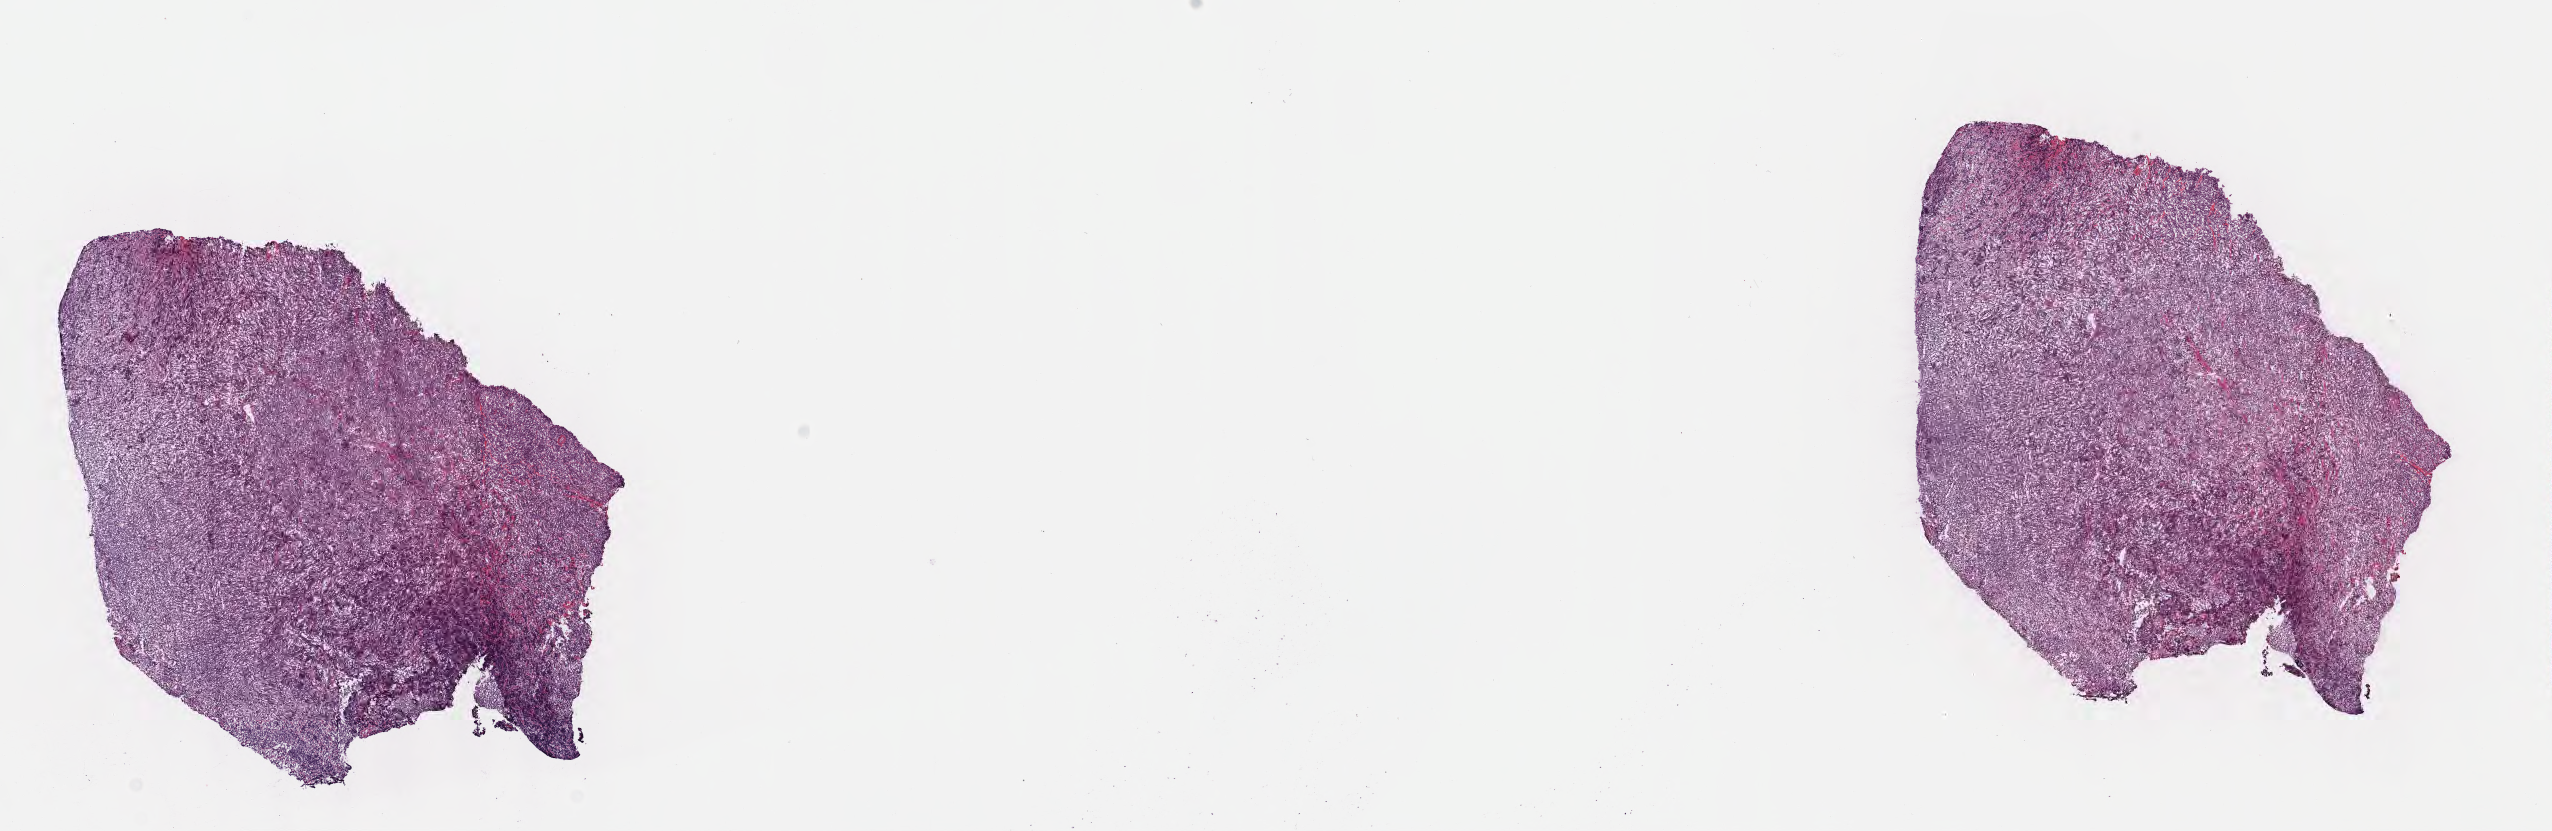
Digitized haematoxylin and eosin-stained section — shown as a low-resolution overview of the whole scanned area (about 20.6 x 6.7 mm). Frozen section. Specimen: primary tumor. Anatomic site: head and neck. Male patient; age at initial diagnosis 4 years. Pathologist review of this section (percent, as recorded): tumor cells 90%, tumor nuclei 95%, stromal cells 10%, necrosis 0%, normal cells 0%. Inflammatory infiltration, as recorded: lymphocyte infiltration 80%, monocyte infiltration 10%, neutrophil infiltration 5%.
• Ann Arbor stage (patient): Stage II
• section: top of the tissue portion
• histologic diagnosis: Burkitt lymphoma, NOS